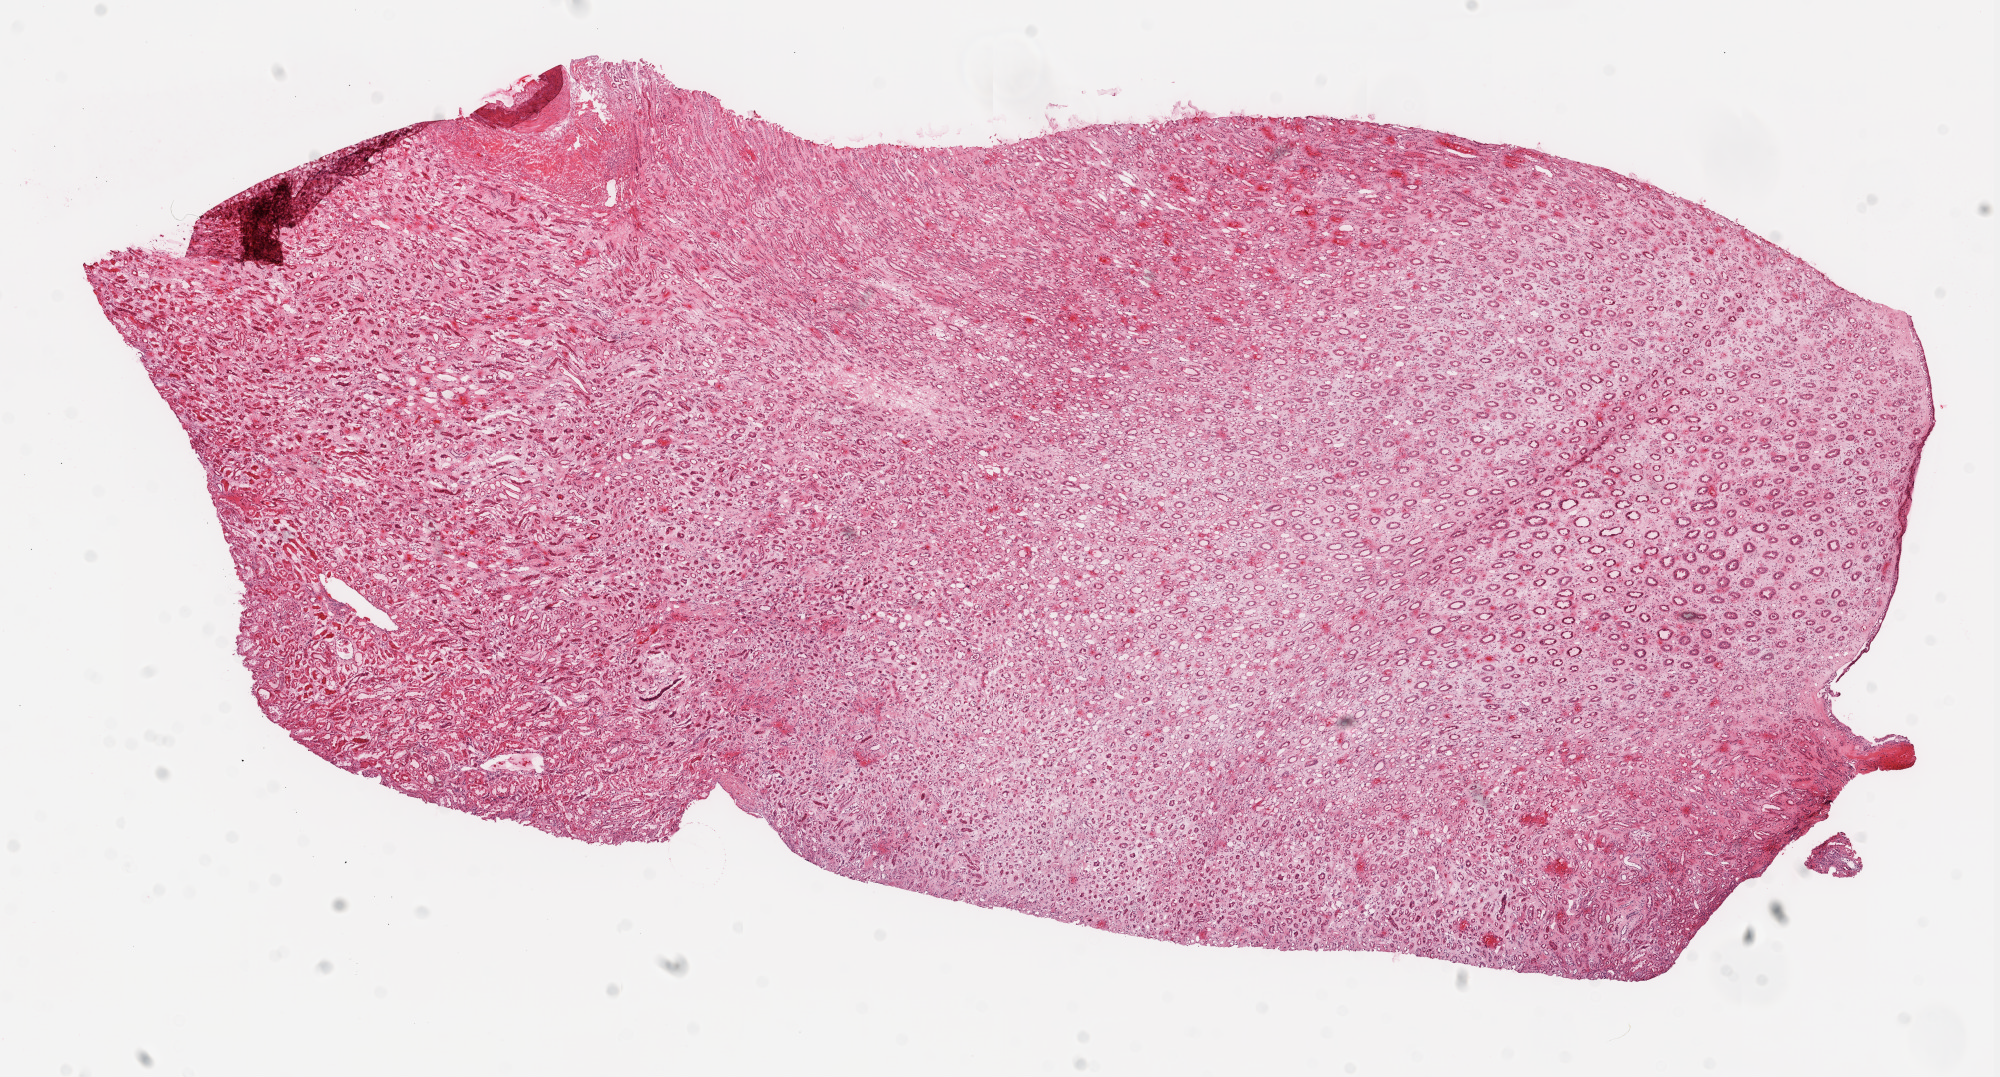
Hematoxylin and eosin (H&E) stained whole-slide image, shown as a low-resolution overview of the whole scanned area (about 16.0 x 8.6 mm). Frozen section from the top of the tissue portion. Kidney, solid tissue normal (non-tumour tissue) sample. Female patient; age at initial diagnosis 86 years.
- this section: solid tissue normal (non-tumour) sample from the same patient
- patient diagnosis: Clear cell adenocarcinoma, NOS